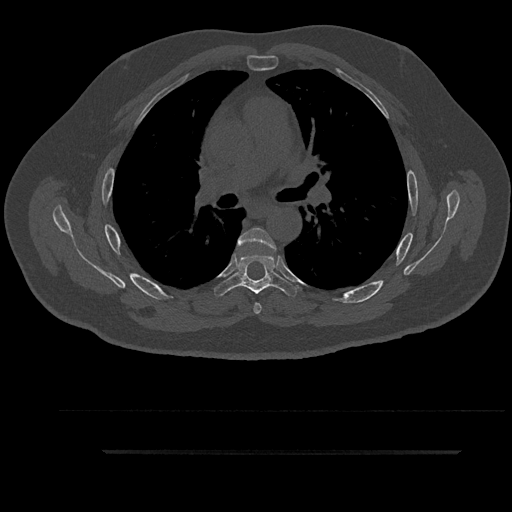
CT including the spine, one axial slice; position 594 of 797 along the scan axis; reconstruction kernel Br40s/3; 120 kVp; bone window (W 1800 / L 400 HU); 512 × 512 image matrix. Patient: male, 63 years. From the clinical record (not read from this slice): primary cancer: renal; vertebrae with lytic lesions (as recorded): T8.
Structures marked on this image (semi-automatically segmented with operator editing):
- T5 vertebra: bounding box (x1, y1, x2, y2) in pixels: (238, 227, 276, 314)
- T6 vertebra: (214, 254, 300, 296)